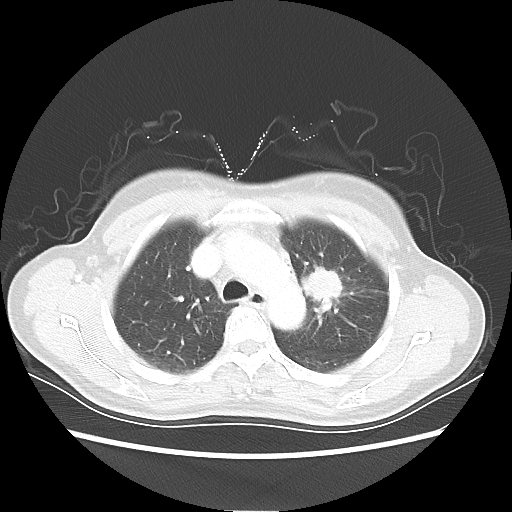
Chest CT, one axial slice. Position 40 of 54 along the scan axis. 80 kVp. Lung window (W 1500 / L -600 HU). 5 mm slice thickness. 512 × 512 image matrix, field of view 360 × 360 mm. Patient: female, 53 years. From the clinical record (not read from this slice): clinical TNM (as recorded): T1c N0 M0.
Outlined on this slice (rectangle marked by the reading radiologist):
- lung tumour (recorded histology: adenocarcinoma): bounding box (x1, y1, x2, y2) in pixels: (296, 258, 350, 307)
- lung tumour (recorded histology: adenocarcinoma): (305, 259, 346, 312)